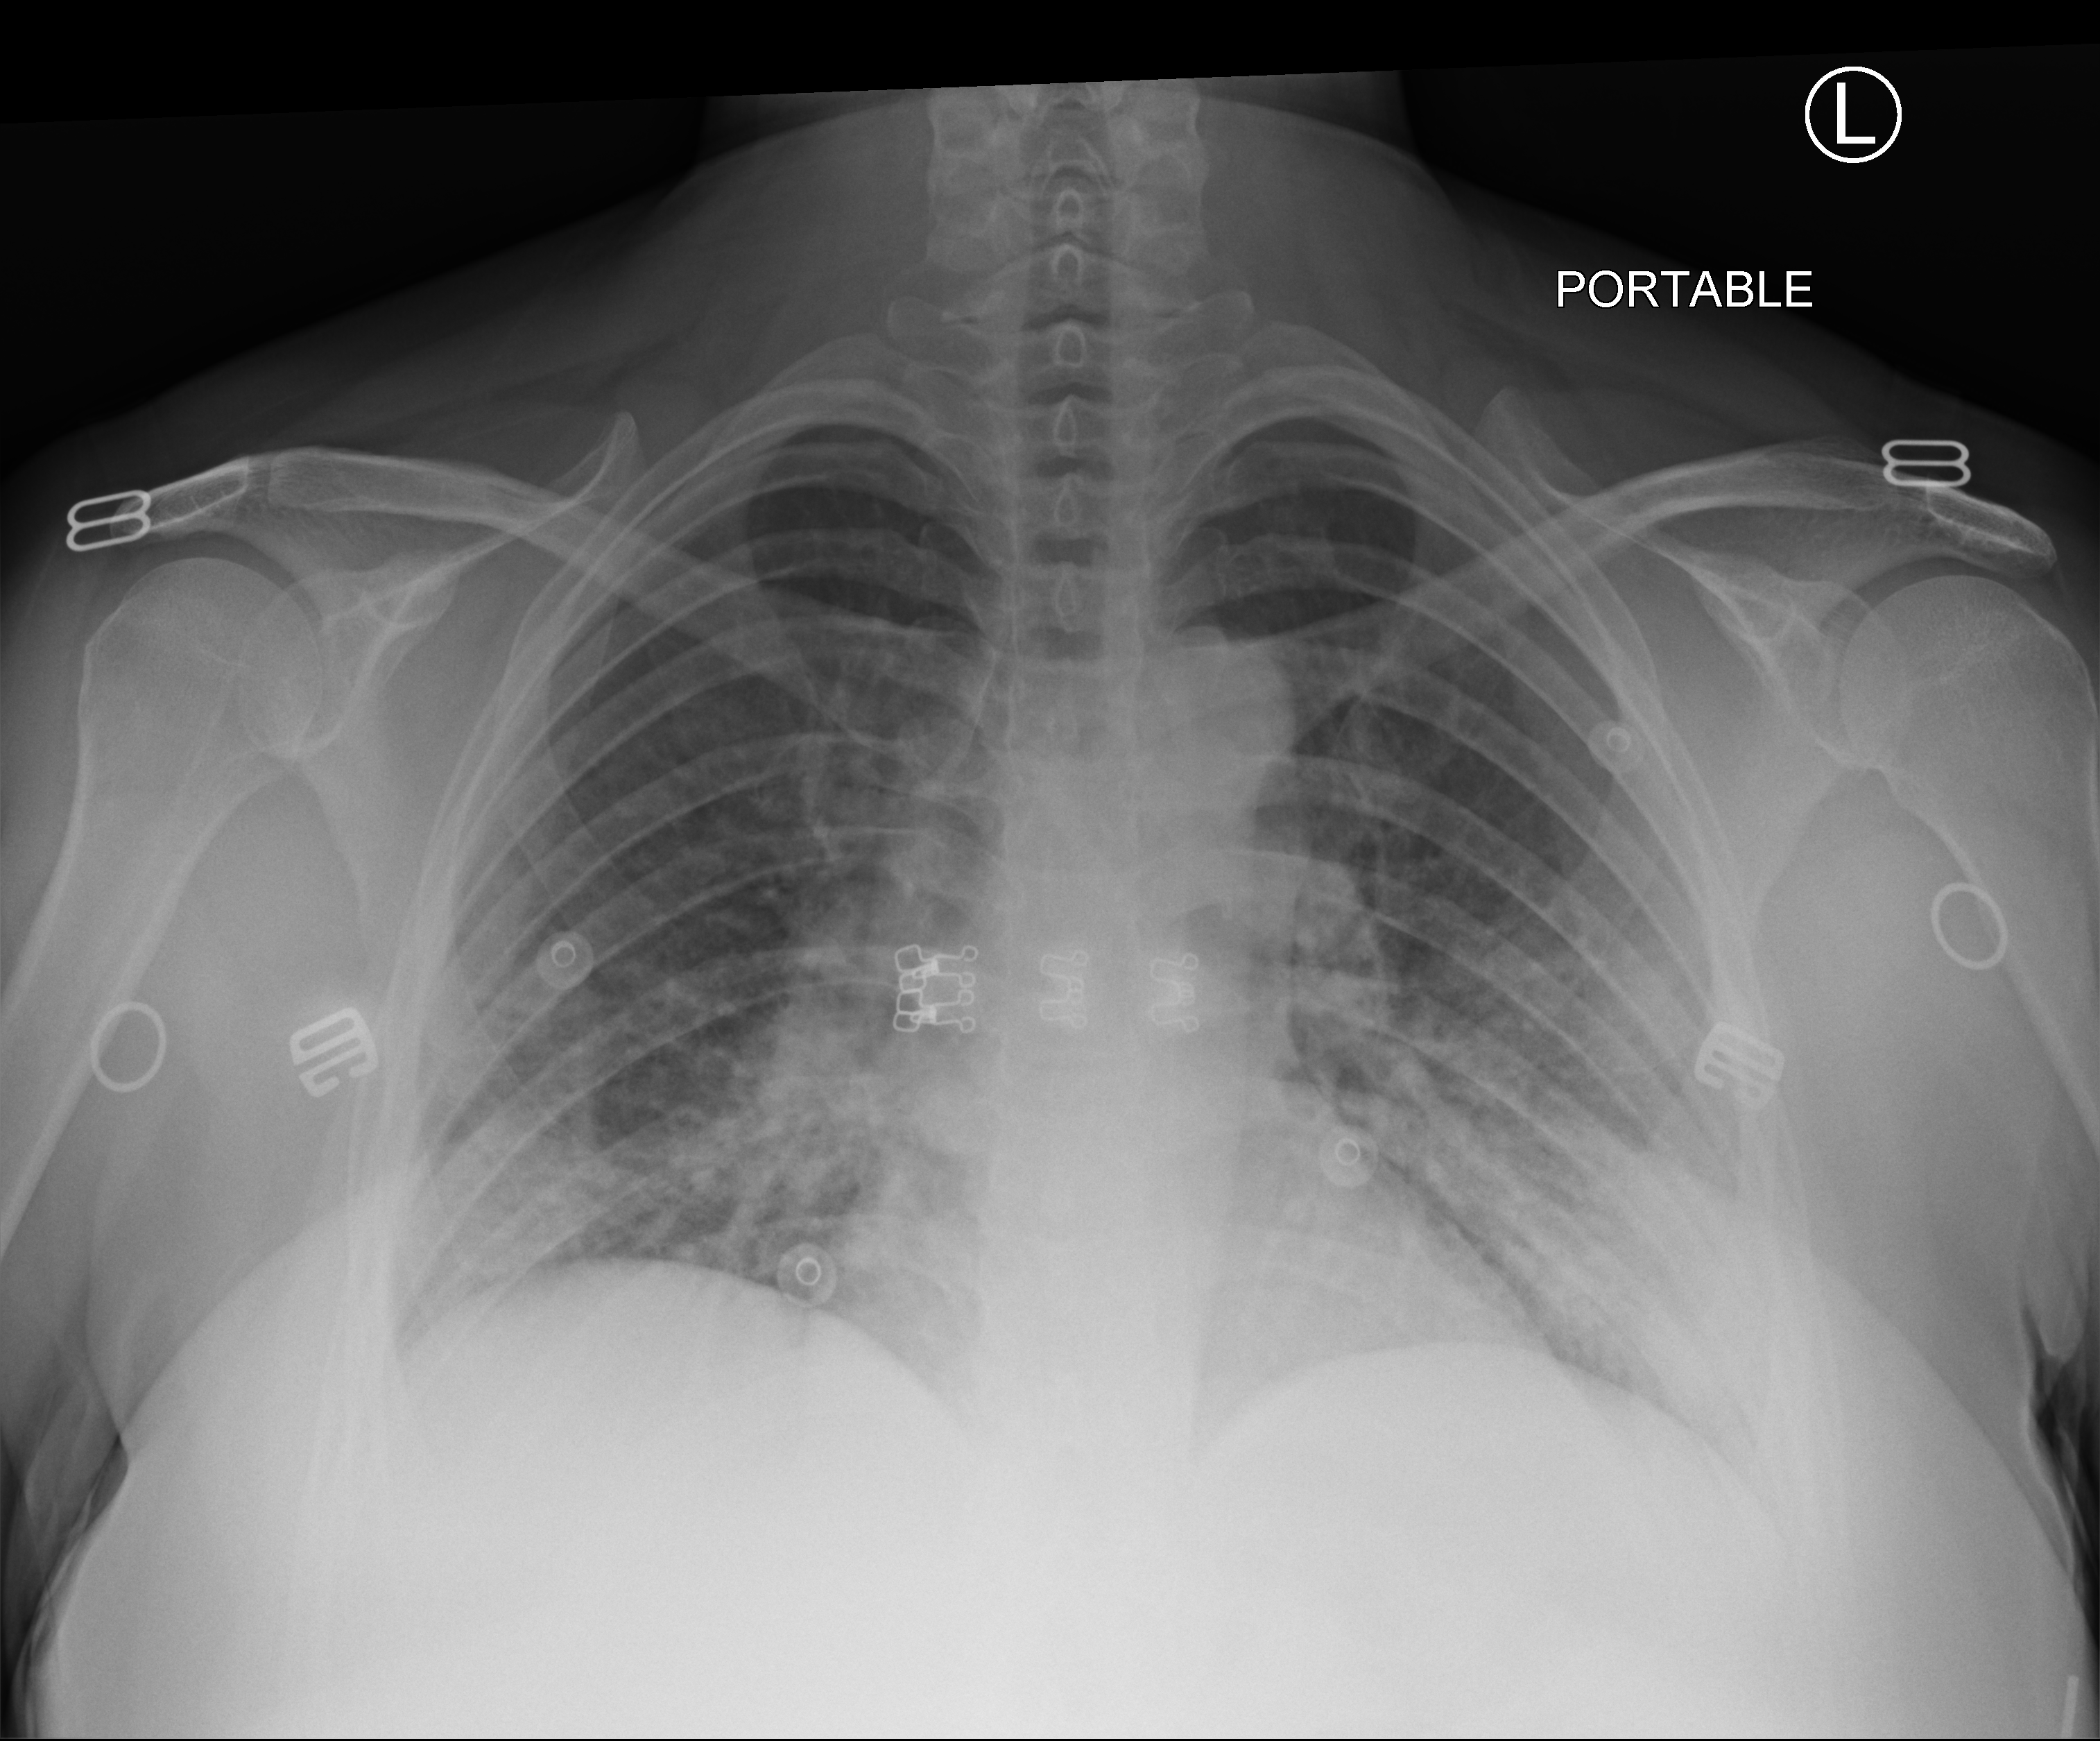
Bedside chest radiograph (computed radiography), anteroposterior (AP) projection. Patient hospitalised with COVID-19; female, aged 18–59 years.
Admission-level facts for this patient (not findings on this image; timing relative to this image not recorded):
- mechanically ventilated during this hospital stay: no
- admitted to intensive care during this hospital stay: no